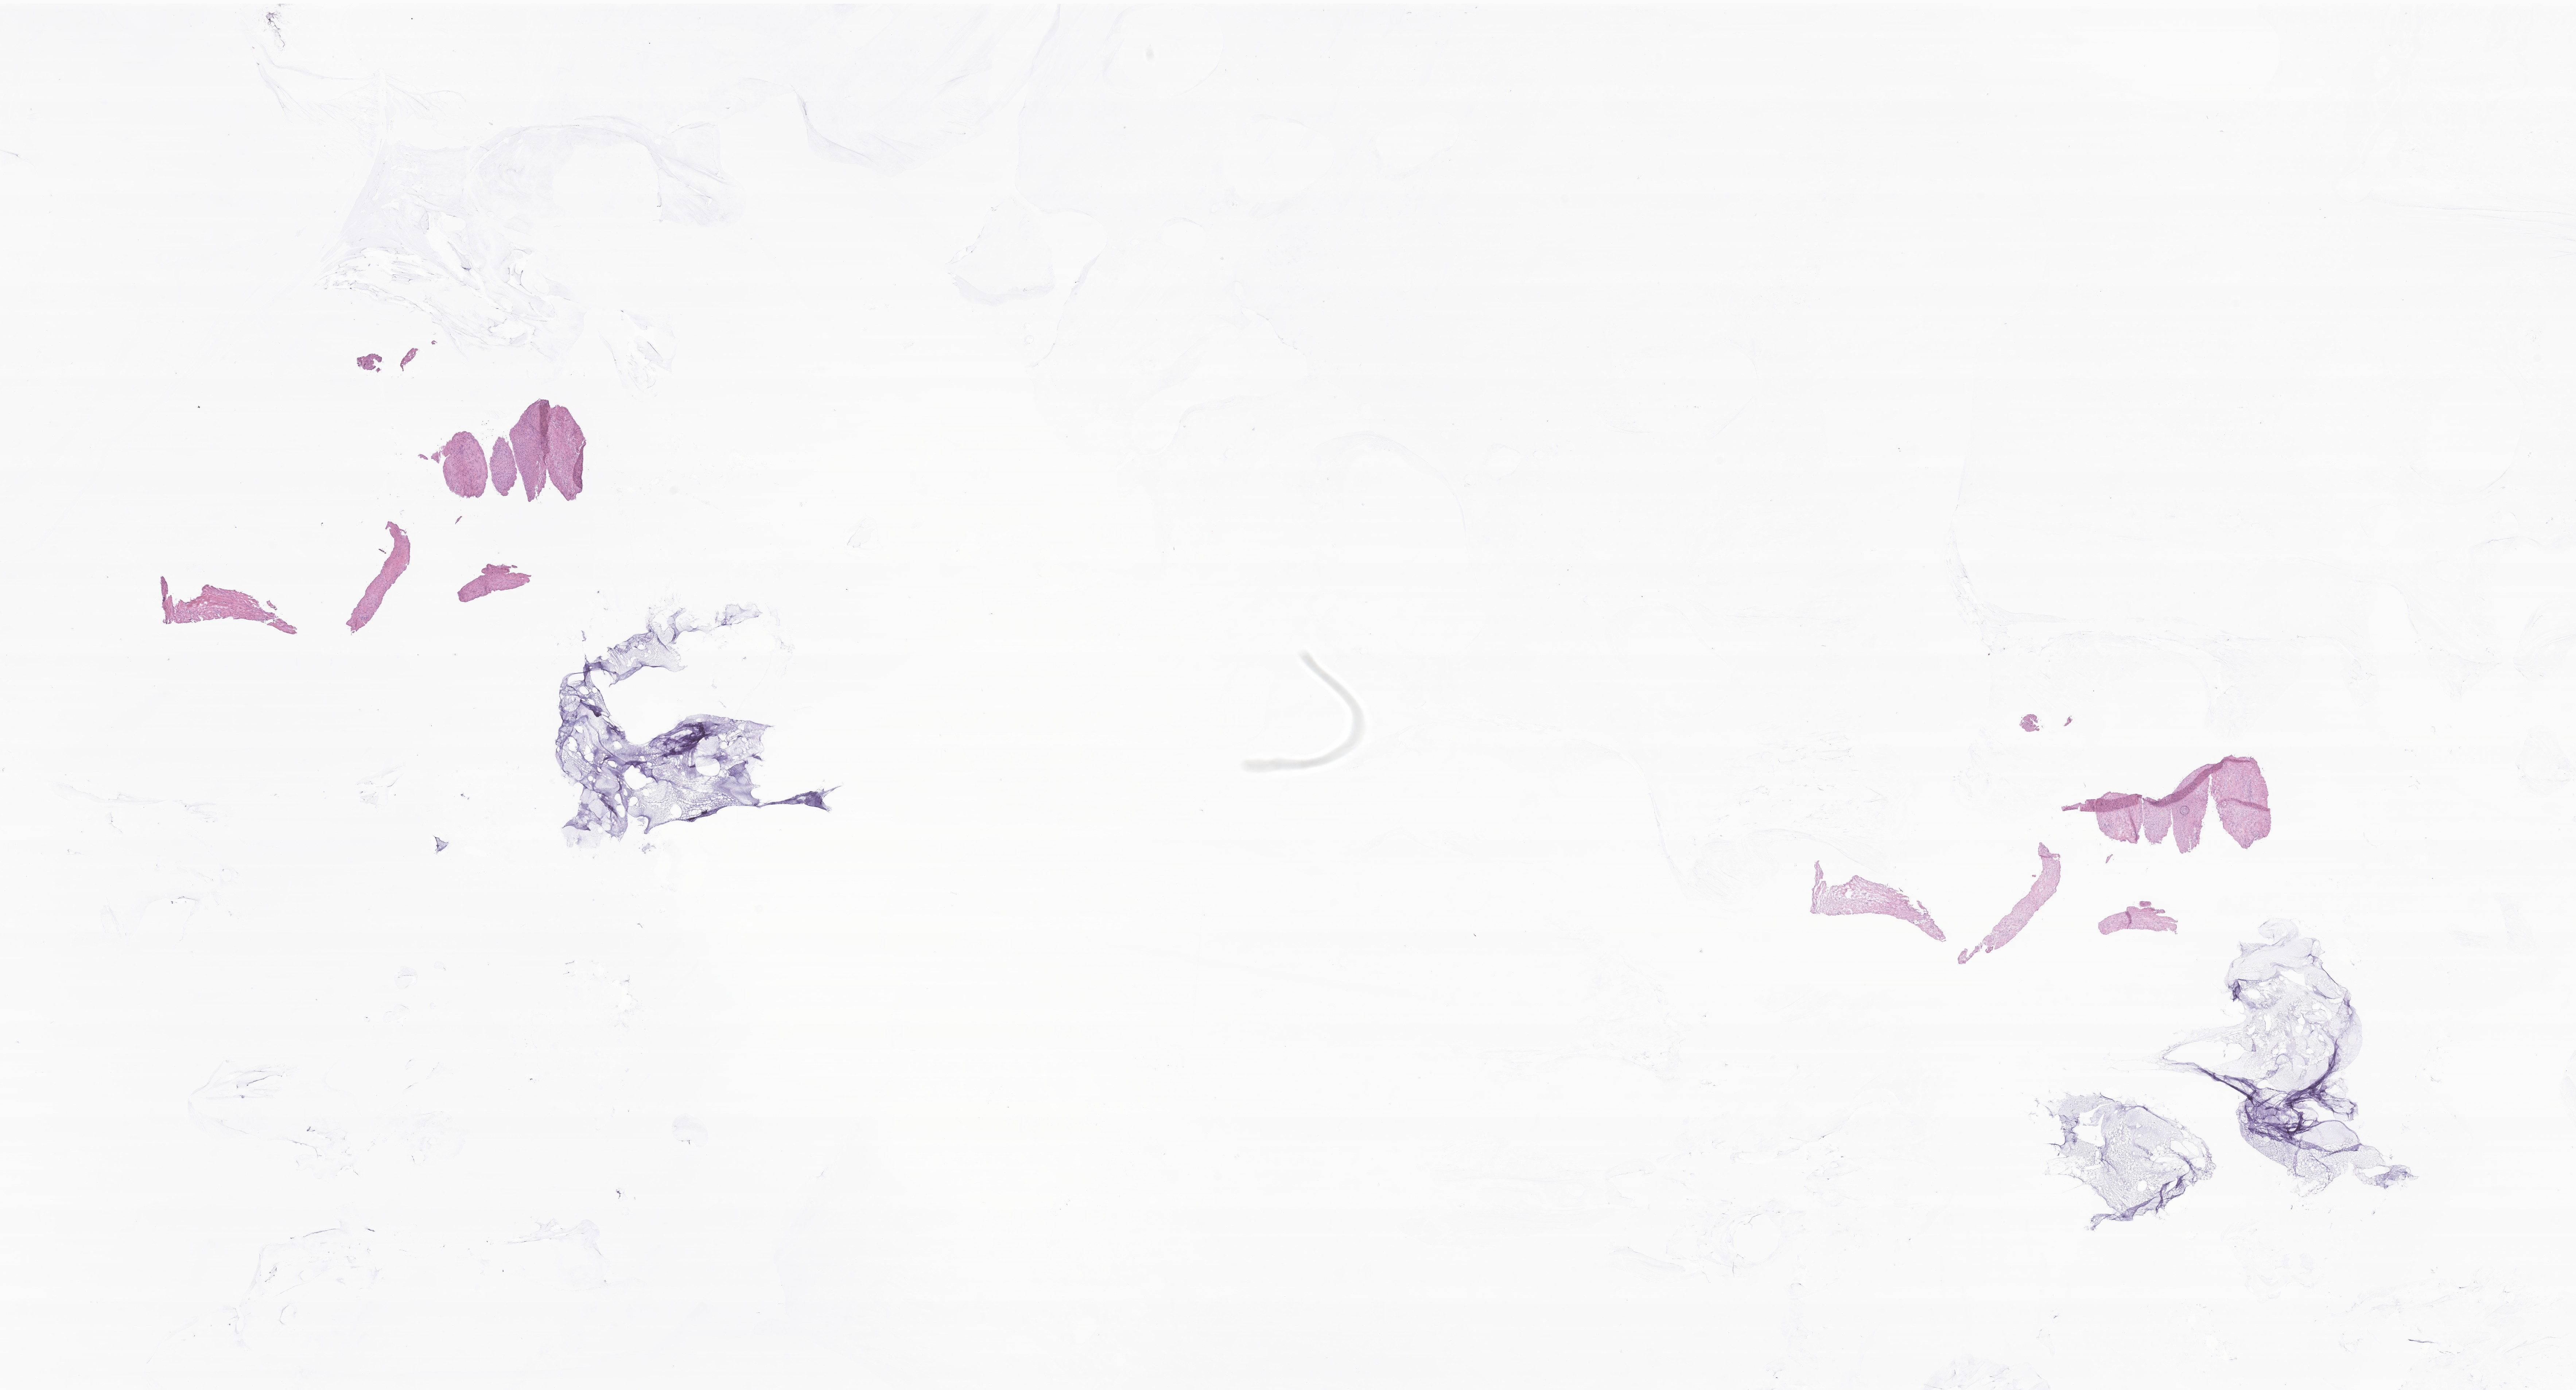
Digitized haematoxylin and eosin-stained section of tumor tissue from the soft tissue of lower extremity — whole scanned area (about 29.8 x 16.1 mm) shown as a low-resolution overview. Cryosection (OCT / tissue freezing medium). Patient male; age 176 months (14 years 8 months).
Diagnosis: Neoplasm, uncertain whether benign or malignant.